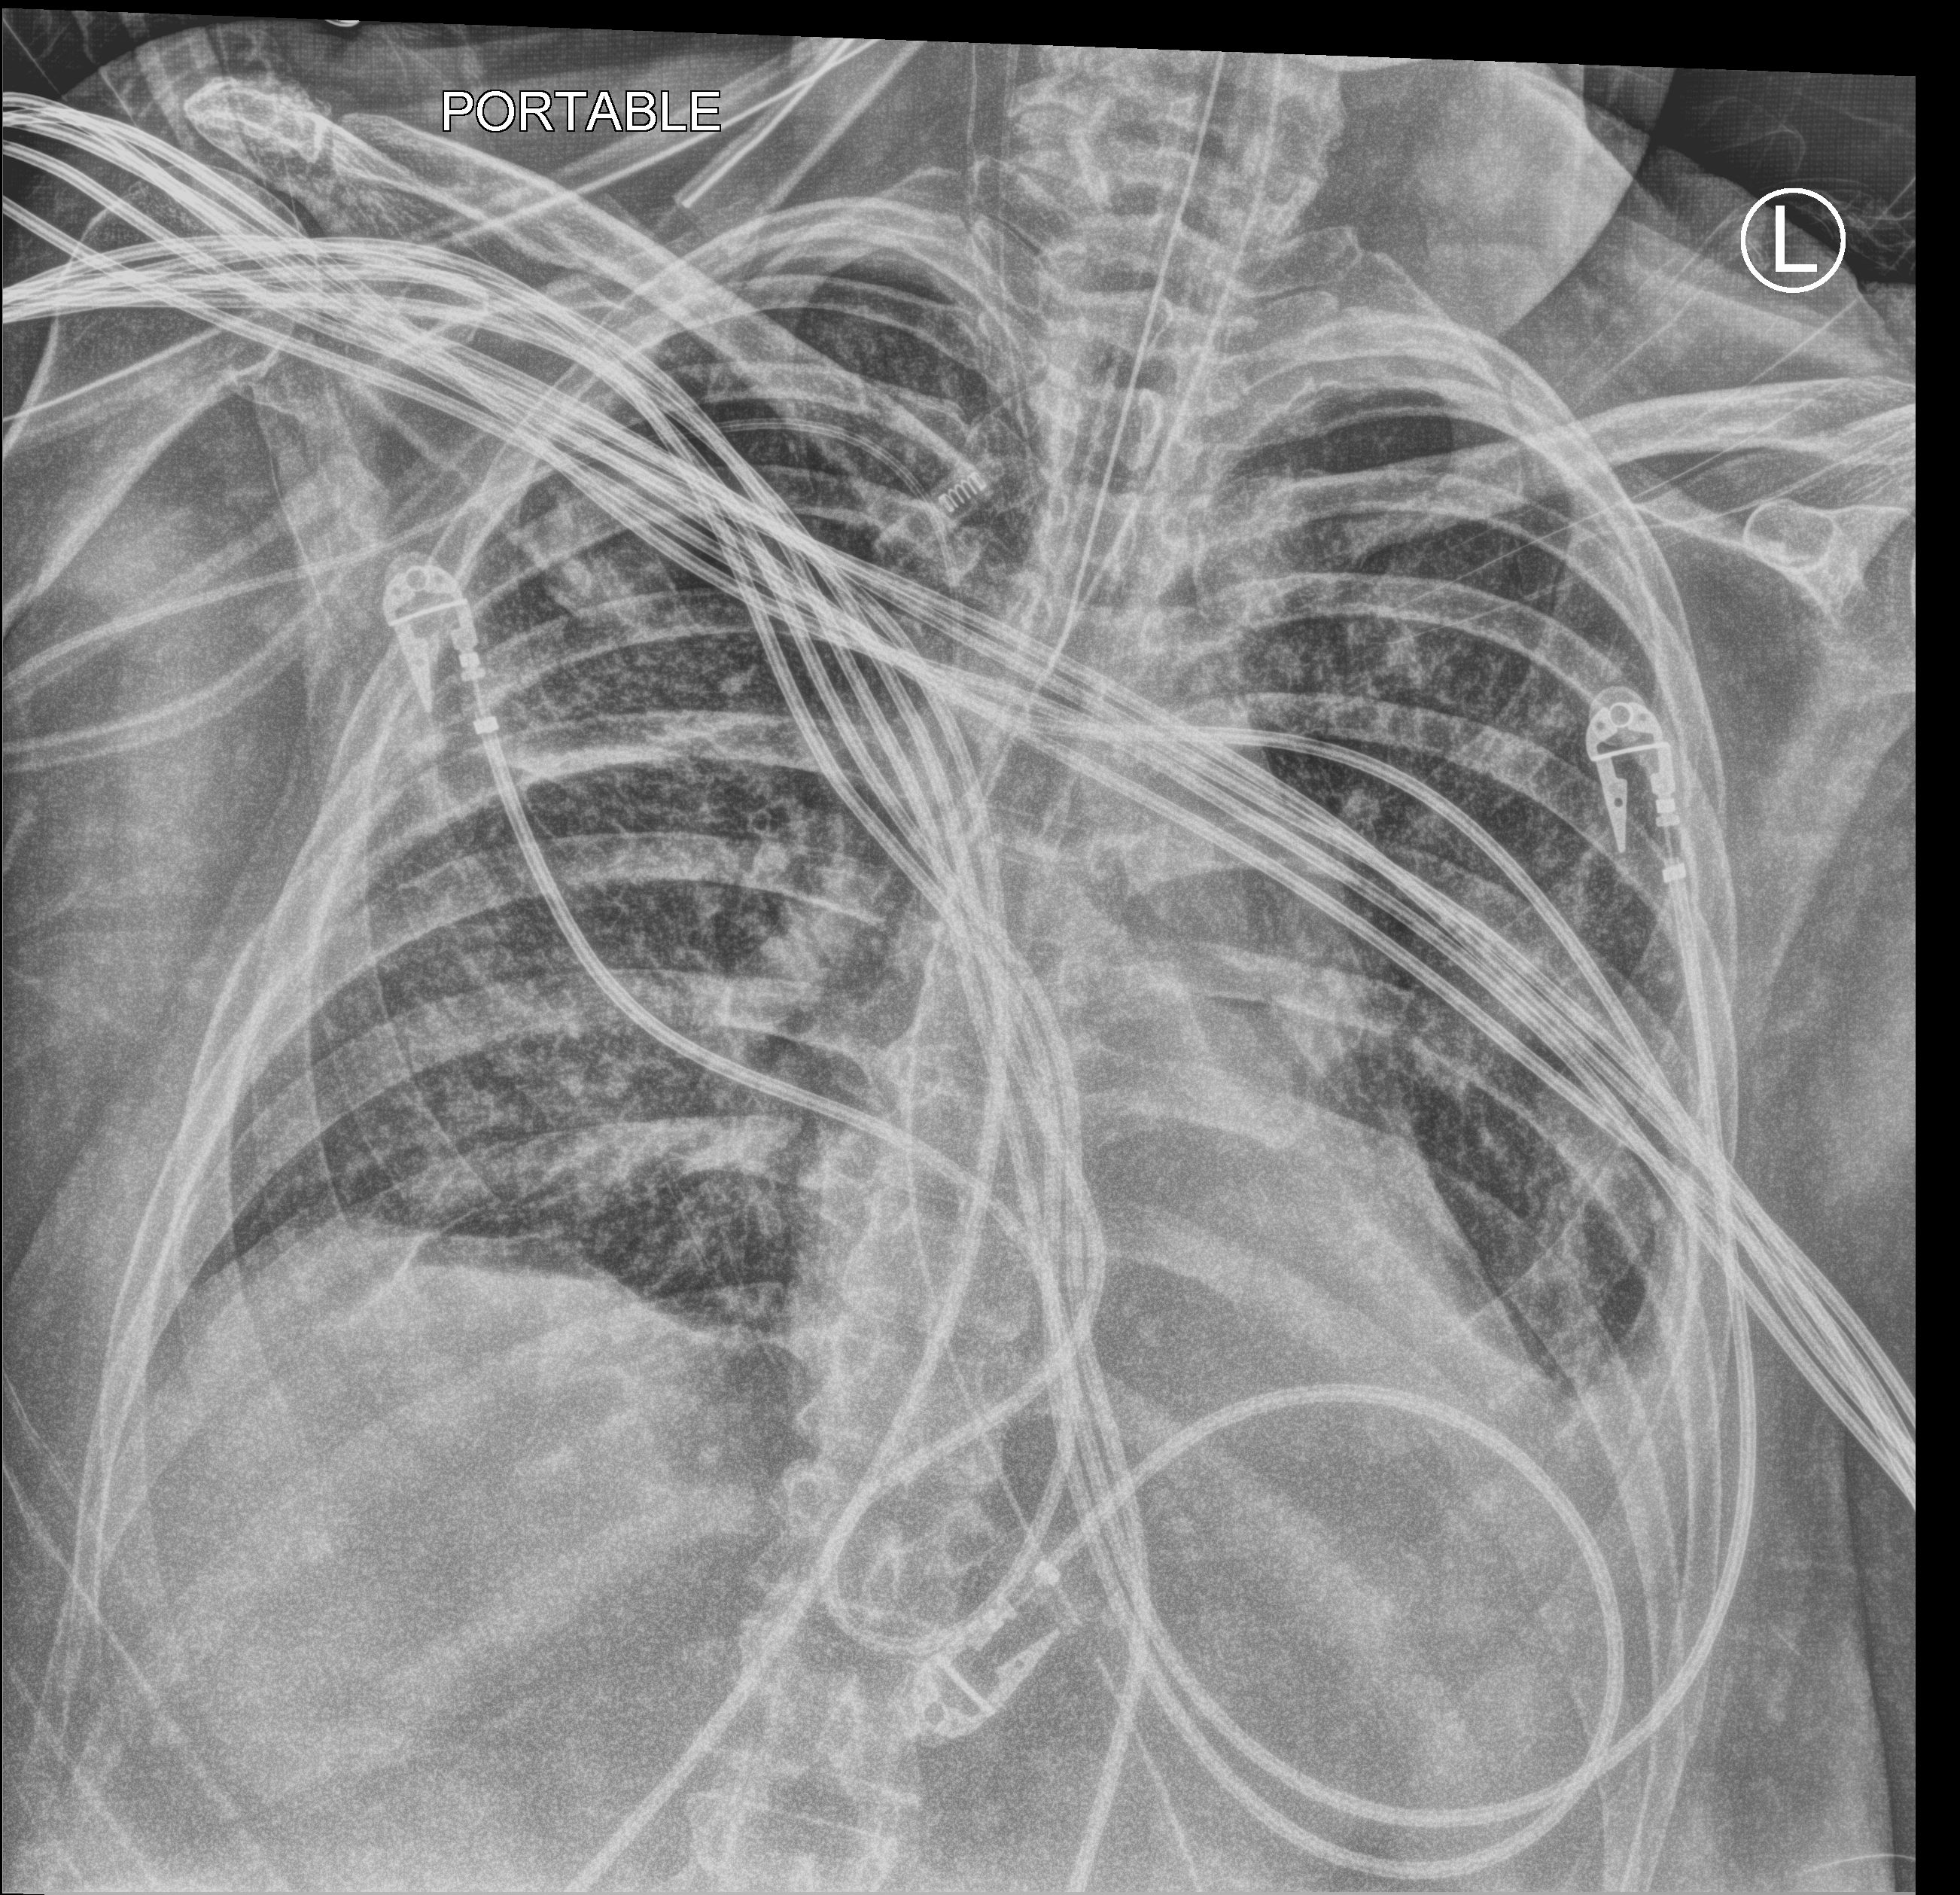
Portable chest radiograph; anteroposterior (AP) projection. Patient hospitalised with COVID-19; female, aged 60–74 years.
From the hospital-stay record, not from the radiograph (when in the stay this image was taken is not recorded):
- admitted to intensive care during this hospital stay: yes
- mechanically ventilated during this hospital stay: yes